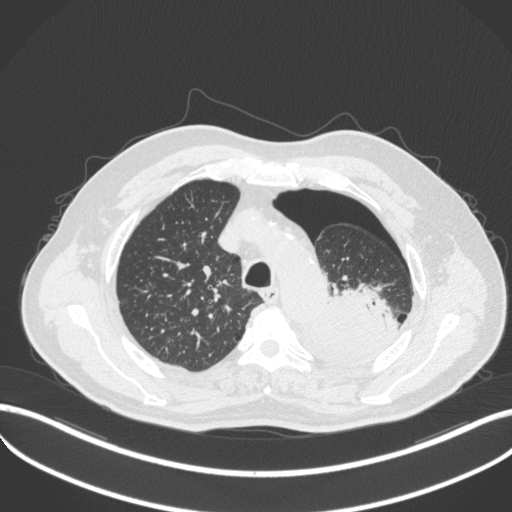
Chest CT, one axial slice; position 390 of 466 along the scan axis; 120 kVp; lung window (W 1500 / L -600 HU); 1 mm slice thickness; 512 × 512 image matrix, field of view 400 × 400 mm. Male patient, age 76 years. Case-level facts recorded for this patient, not image findings: clinical TNM (as recorded): T3 N0 M1b.
Structures marked on this image (bounding box drawn by a radiologist):
- lung tumour (recorded histology: adenocarcinoma): bounding box [x1, y1, x2, y2] px = [311, 283, 392, 368]